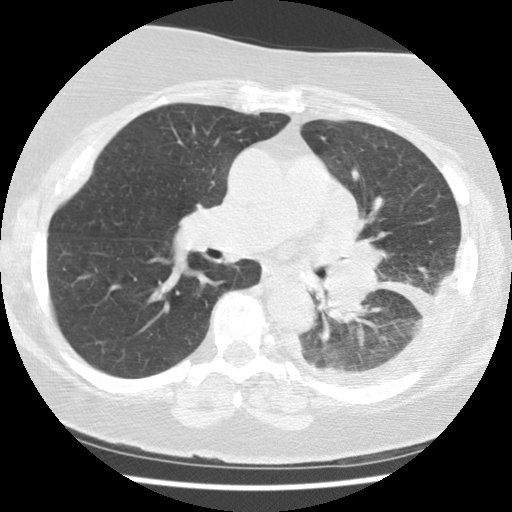
Chest CT (low-dose screening protocol), one axial image, baseline screening round, lung window (W 1500 / L -600 HU), 2.5 mm slice thickness, standard (soft-tissue) reconstruction kernel (STANDARD), 120 kVp, slice 51 of 114 in the series, 512 × 512 image matrix, field of view 320 × 320 mm. Female participant, aged 65 years at enrolment. Current smoker at enrolment.
Expert-annotated lung lesion, bounding box <293,282,387,354> (left, top, right, bottom; pixels). The exam's reader record, not a measurement of the box and not confirmed to be the same lesion: non-calcified nodule or mass ≥4 mm, left lower lobe, 74 × 48 mm, spiculated (stellate) margins, soft tissue attenuation. Participant outcome: lung cancer diagnosed 13 days after this screen — adenocarcinoma, NOS, left lower lobe, stage IV (AJCC 6th edition), 74 mm at pathology.